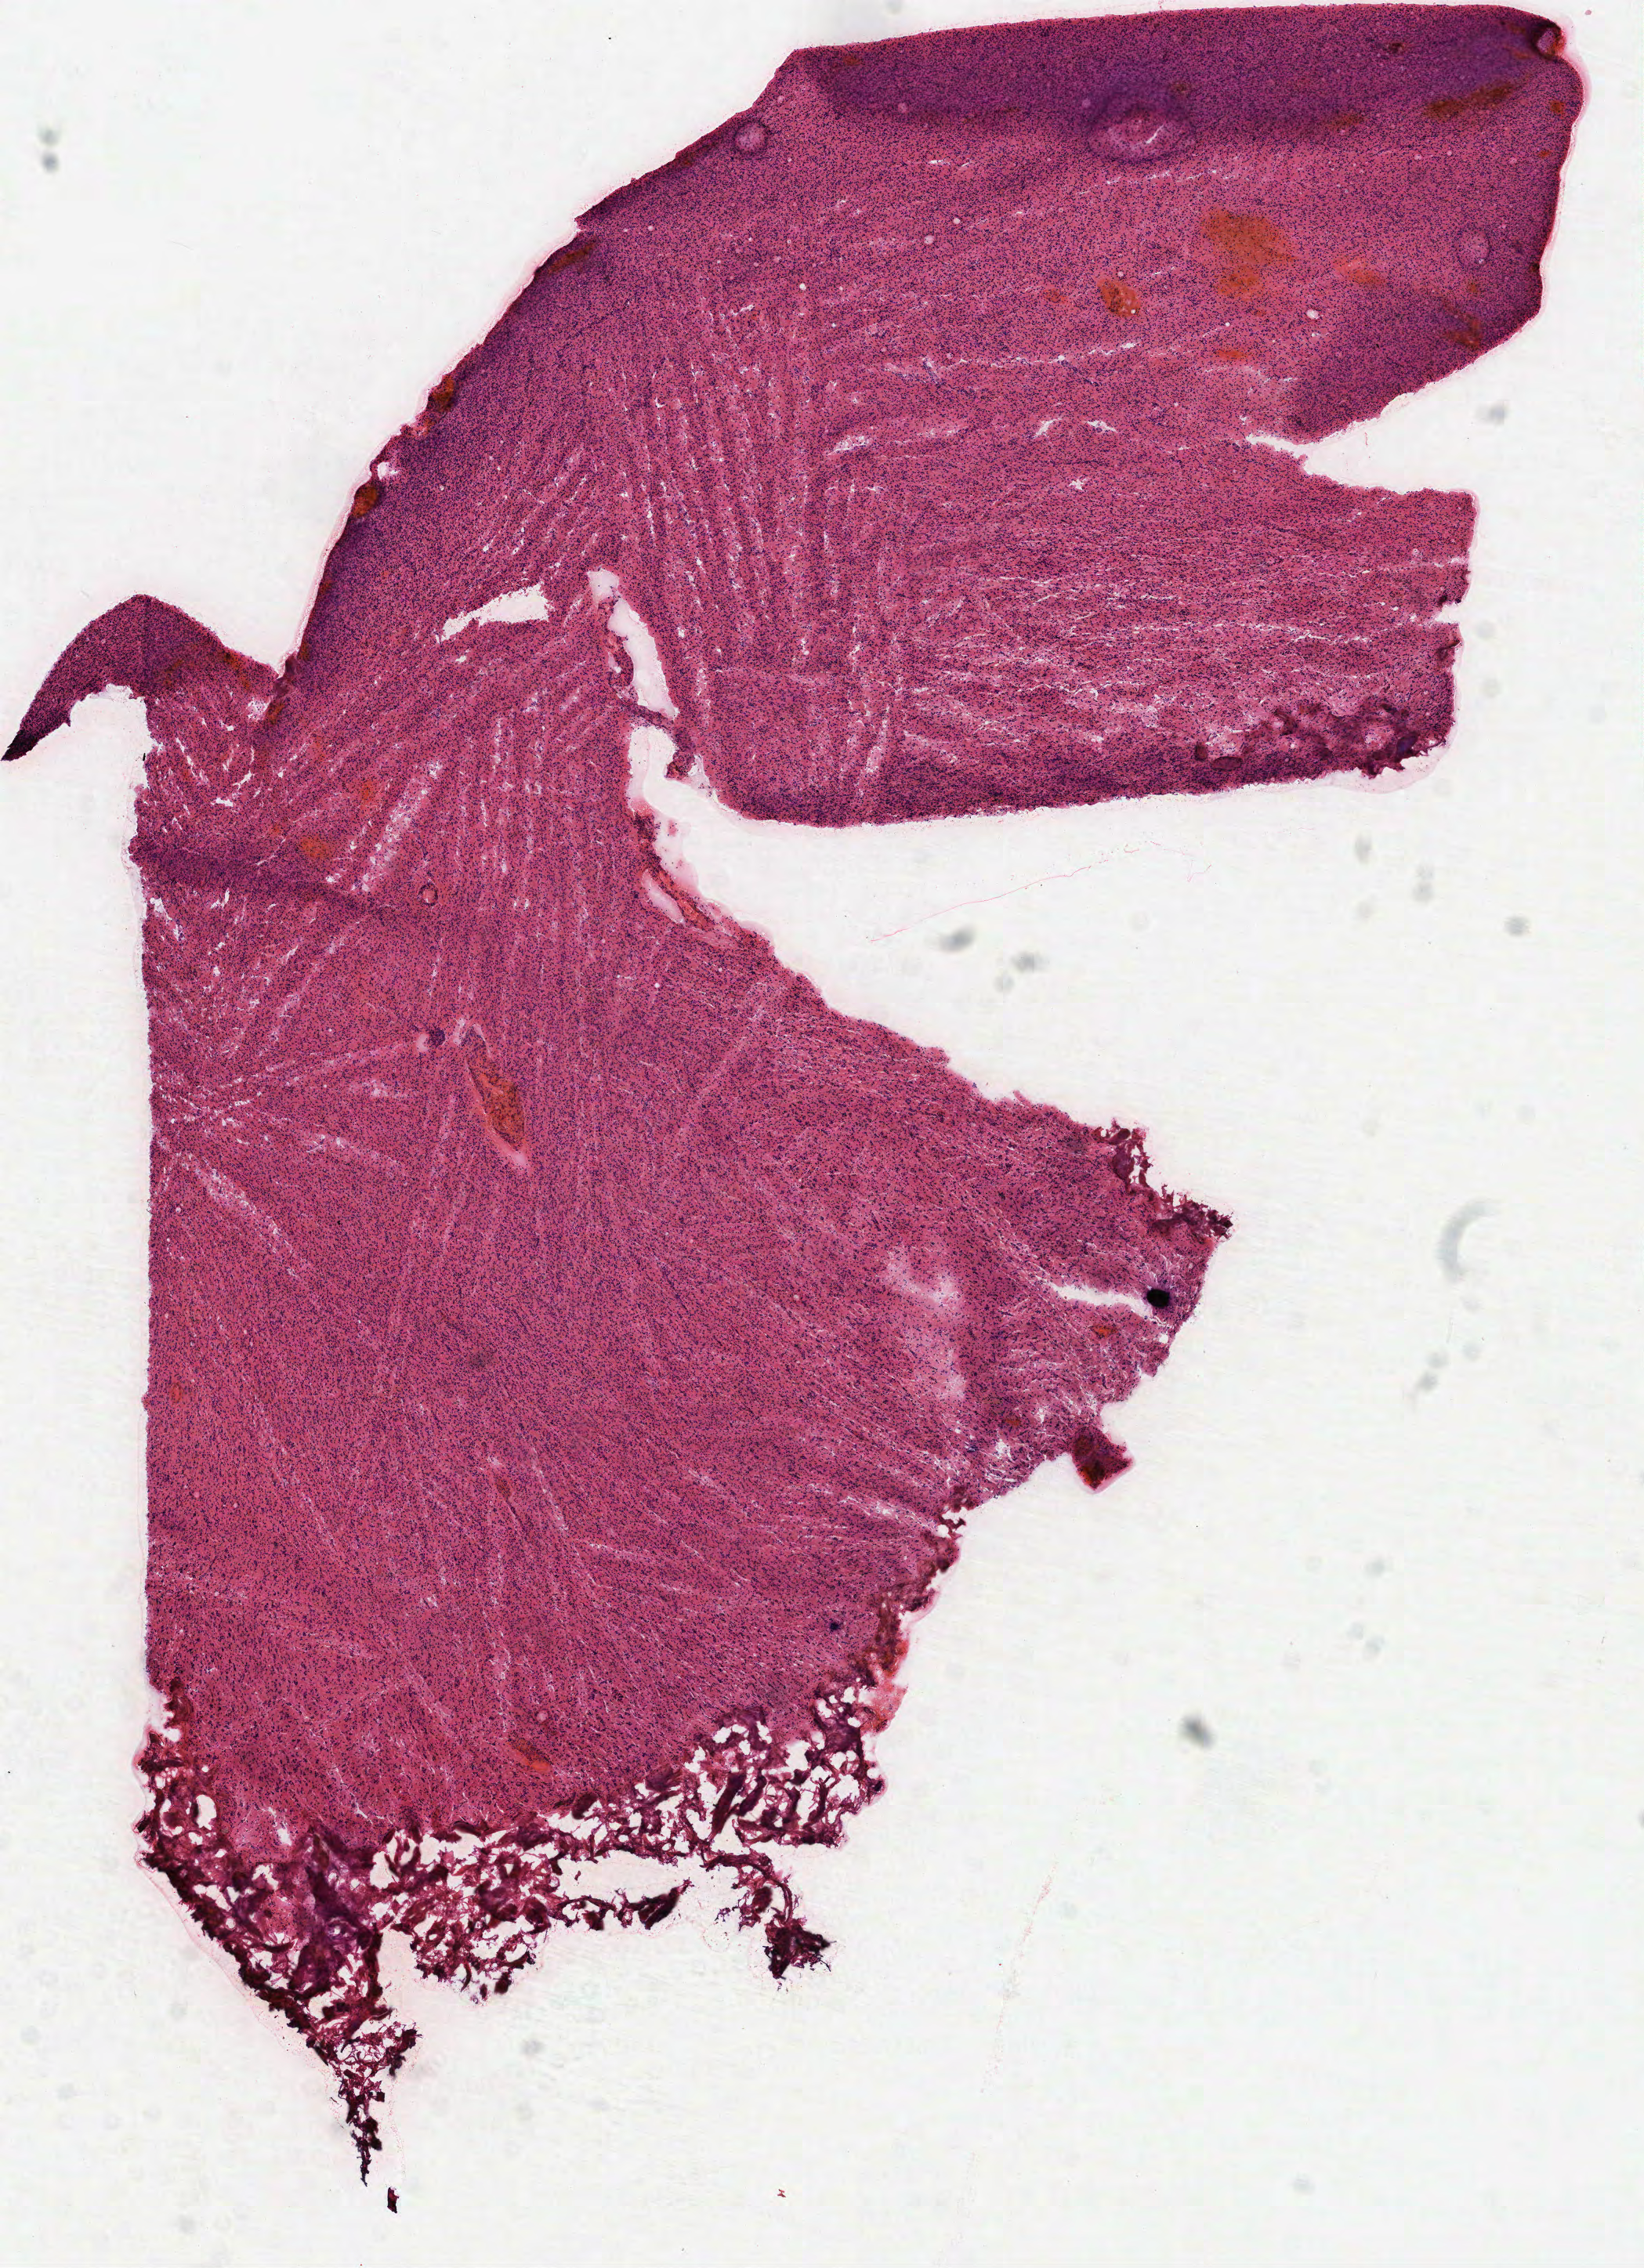
H&E whole-slide image, whole scanned area (about 8.5 x 11.7 mm, from a 40x scan) shown as a low-resolution overview; frozen section from the top of the tissue portion; primary tumour sample from the brain. Male patient; age at initial diagnosis 37 years. Histologic grade: G2 (moderately differentiated). Composition of this section per pathologist review: tumour cells 100%, tumour nuclei 85%, normal cells 0%, stromal cells 0%, necrosis 0%.
* histologic diagnosis: Oligodendroglioma, NOS (cerebrum)
* laterality: right